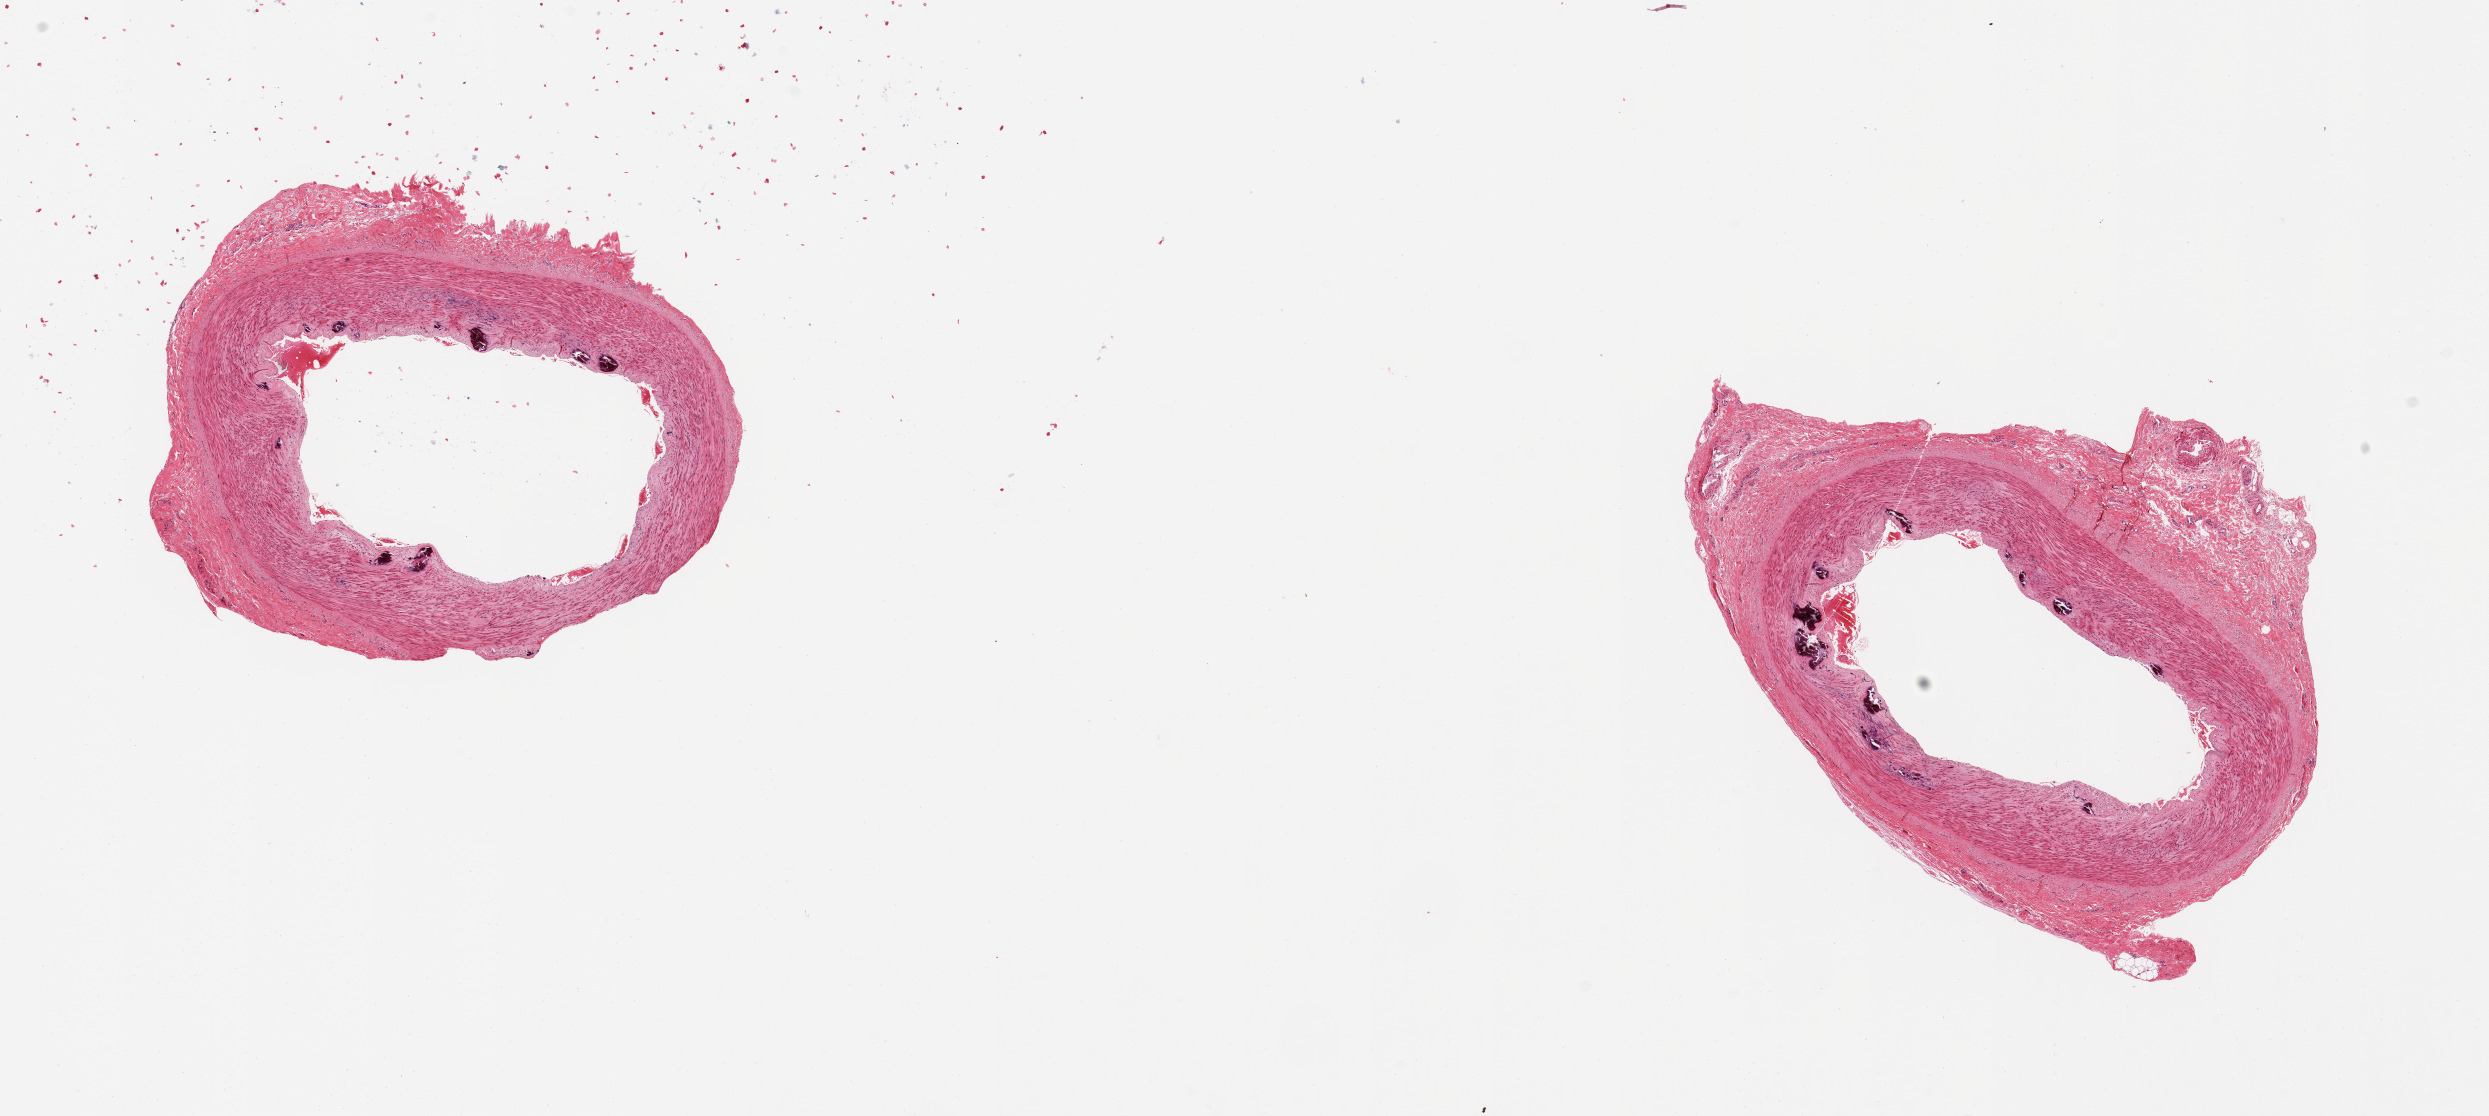
Whole-slide image, haematoxylin and eosin stain, brightfield — shown as a low-resolution overview of the whole scanned area (about 19.7 x 8.8 mm); PAXgene-fixed, paraffin-embedded tissue; section of tibial artery (target tissue); donor tissue sample. Donor sex: male.
- pathologist's review note for this sample: 2 pieces, adherent nubbin of fibrous tissue up to ~1mm